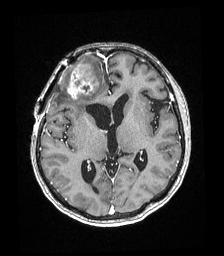
Brain MRI from a brain-tumour surgery series, one axial slice. Slice 99 of 192 in the series (ordered by position). T1-weighted post-contrast. 1 mm slice thickness. 224 × 256 image matrix. Case-level facts recorded for this patient, not image findings: histopathology: Astrocytoma; WHO grade: 4; IDH mutation: yes.
Annotated regions visible in this slice (outlined manually by an expert reader):
- tumour: bounding box <68,60,98,99> (left, top, right, bottom; pixels)